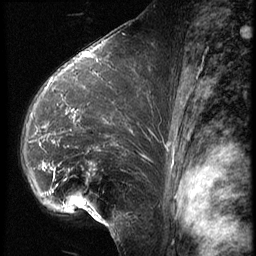
Breast MRI (dynamic contrast-enhanced), one sagittal slice; position 38 of 62 along the scan axis; 3 images stored at this slice position (order not interpretable as contrast timing); 1.5 T; TE 4.2 ms, TR 9 ms; 2.5 mm slice thickness; 256 × 256 image matrix. Patient: female, 39 years. From the clinical record (not read from this slice): setting: breast cancer imaged before/during neoadjuvant chemotherapy; receptor status: HER2-positive.
Structures marked on this image (semi-automatic segmentation, software-assisted and operator-edited):
- analysis volume of interest (the breast-tissue region the enhancement analysis was run in; not a lesion): bounding box (x1, y1, x2, y2) in pixels: (19, 64, 157, 228)
- tumour enhancement mask (voxels above the 140 % enhancement threshold inside the analysis volume of interest): (39, 123, 115, 188)